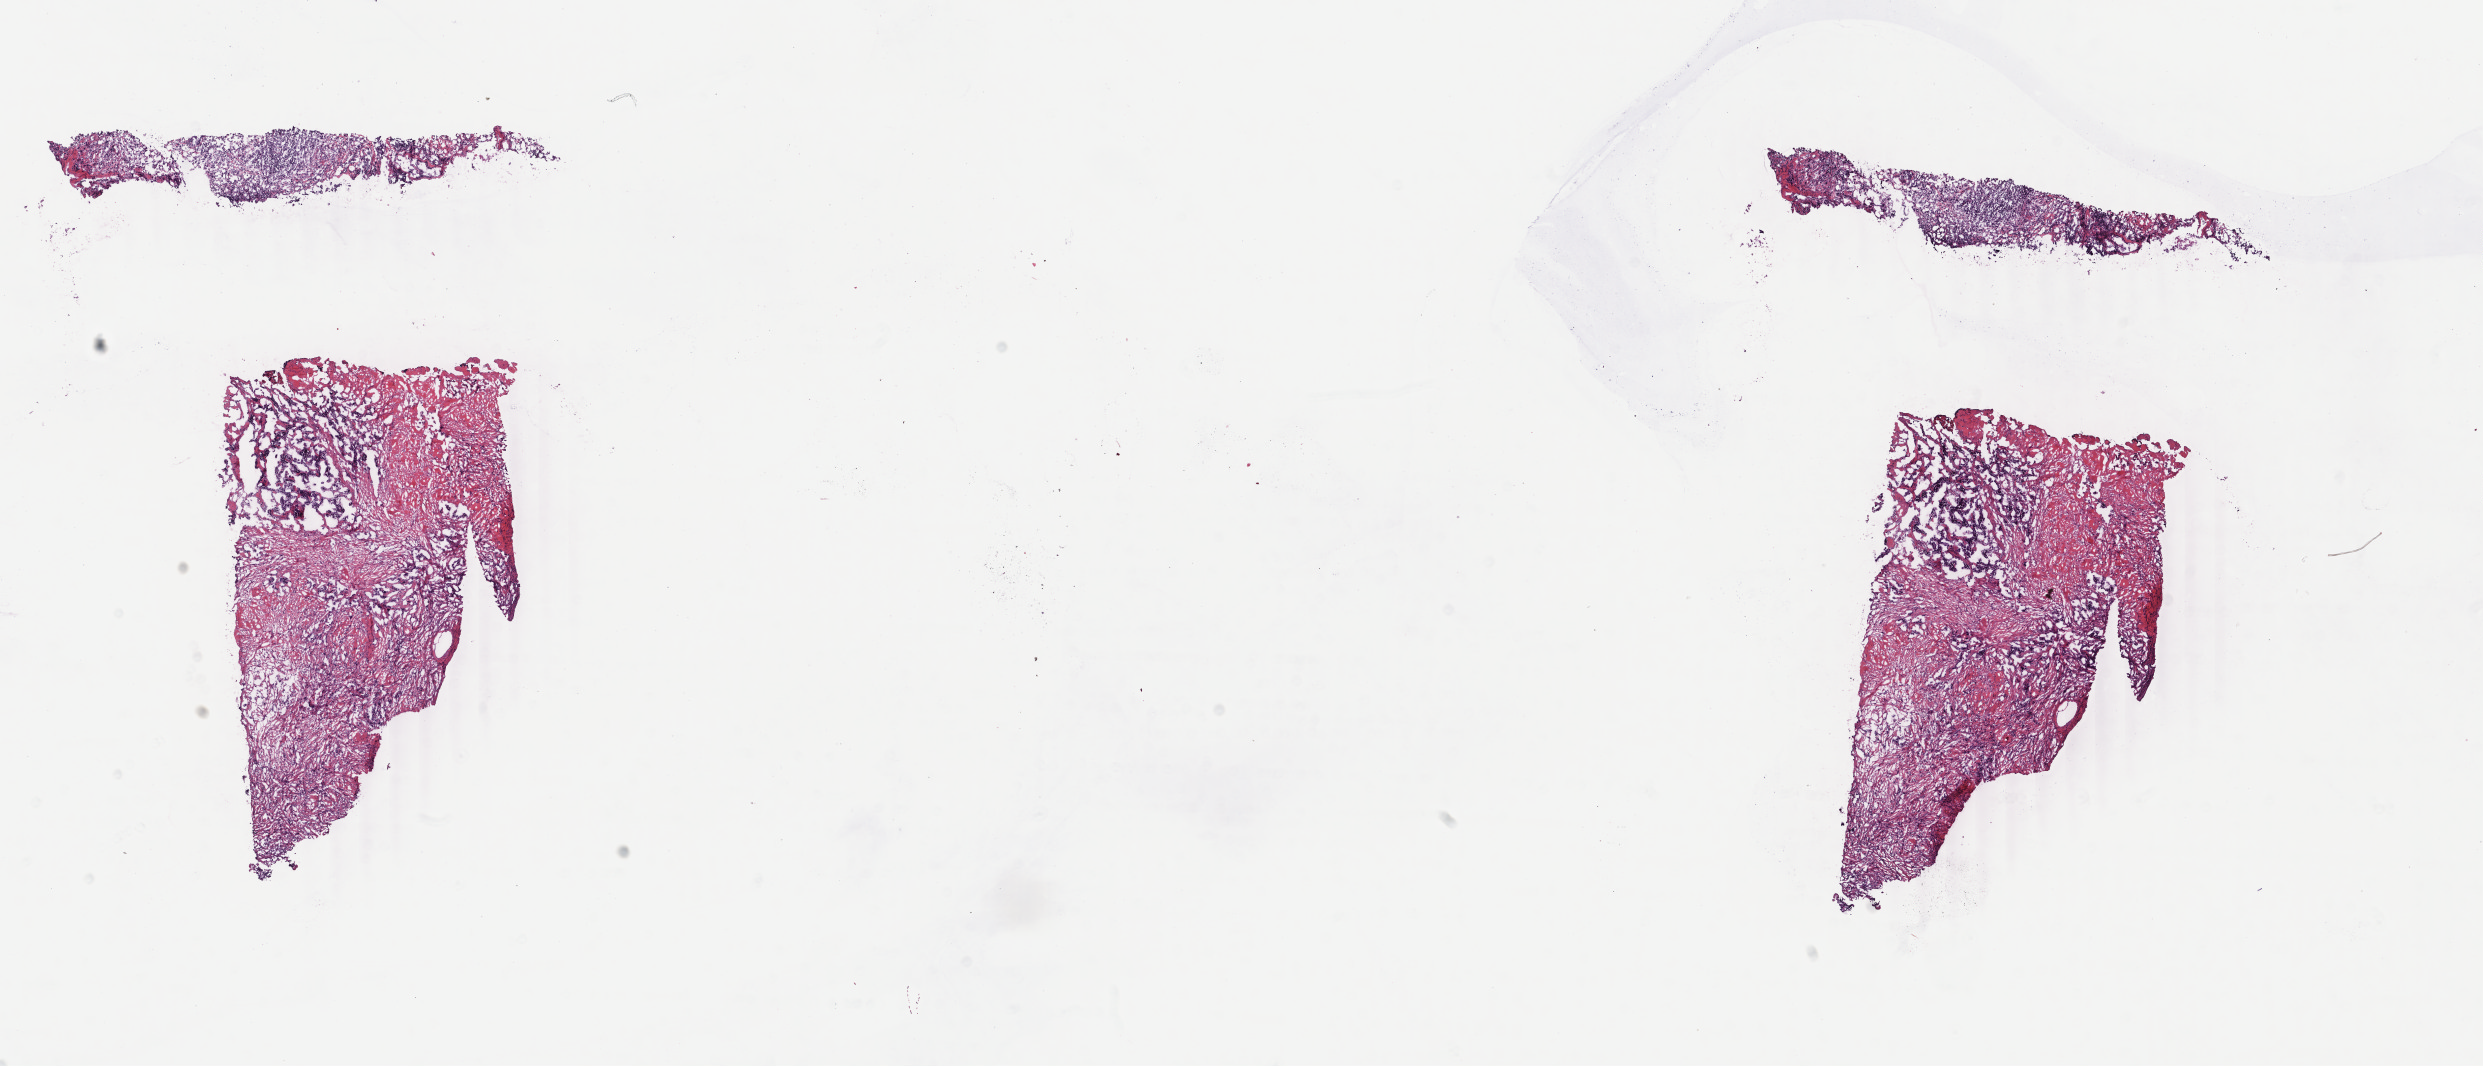
Whole-slide histology image, H&E-stained, shown as a low-resolution overview of the whole scanned area (about 19.8 x 8.5 mm, slide scanned at 40x), frozen section, sample: primary tumour, breast. Female, age 39 years at initial diagnosis. Slide review estimates, as recorded: tumour cells 40%, tumour nuclei 60%, normal cells 0%, stromal cells 60%, necrosis 0%. Infiltration values recorded for this section: lymphocyte infiltration 0%, monocyte infiltration 0%, neutrophil infiltration 0%.
Lymph nodes positive (case pathology): 1 of 23 examined. AJCC pathologic stage: IIIA (4th edition). Histologic diagnosis: Infiltrating duct carcinoma, NOS. Laterality: right.